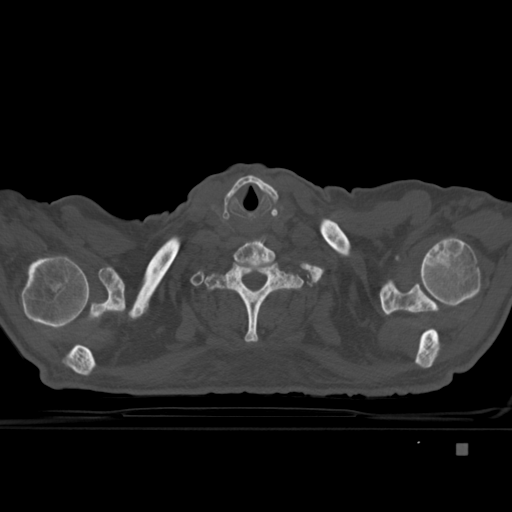
CT including the spine, one axial slice. Slice 361 of 451 in the series (ordered by position). Bone window (W 1800 / L 400 HU). 512 × 512 image matrix, field of view 378 × 378 mm. Male patient, age 75 years. From the clinical record (not read from this slice): primary cancer: prostate.
Outlined on this slice (semi-automatic segmentation, software-assisted and operator-edited):
- T1 vertebra: bounding box [x1, y1, x2, y2] px = [203, 259, 304, 342]